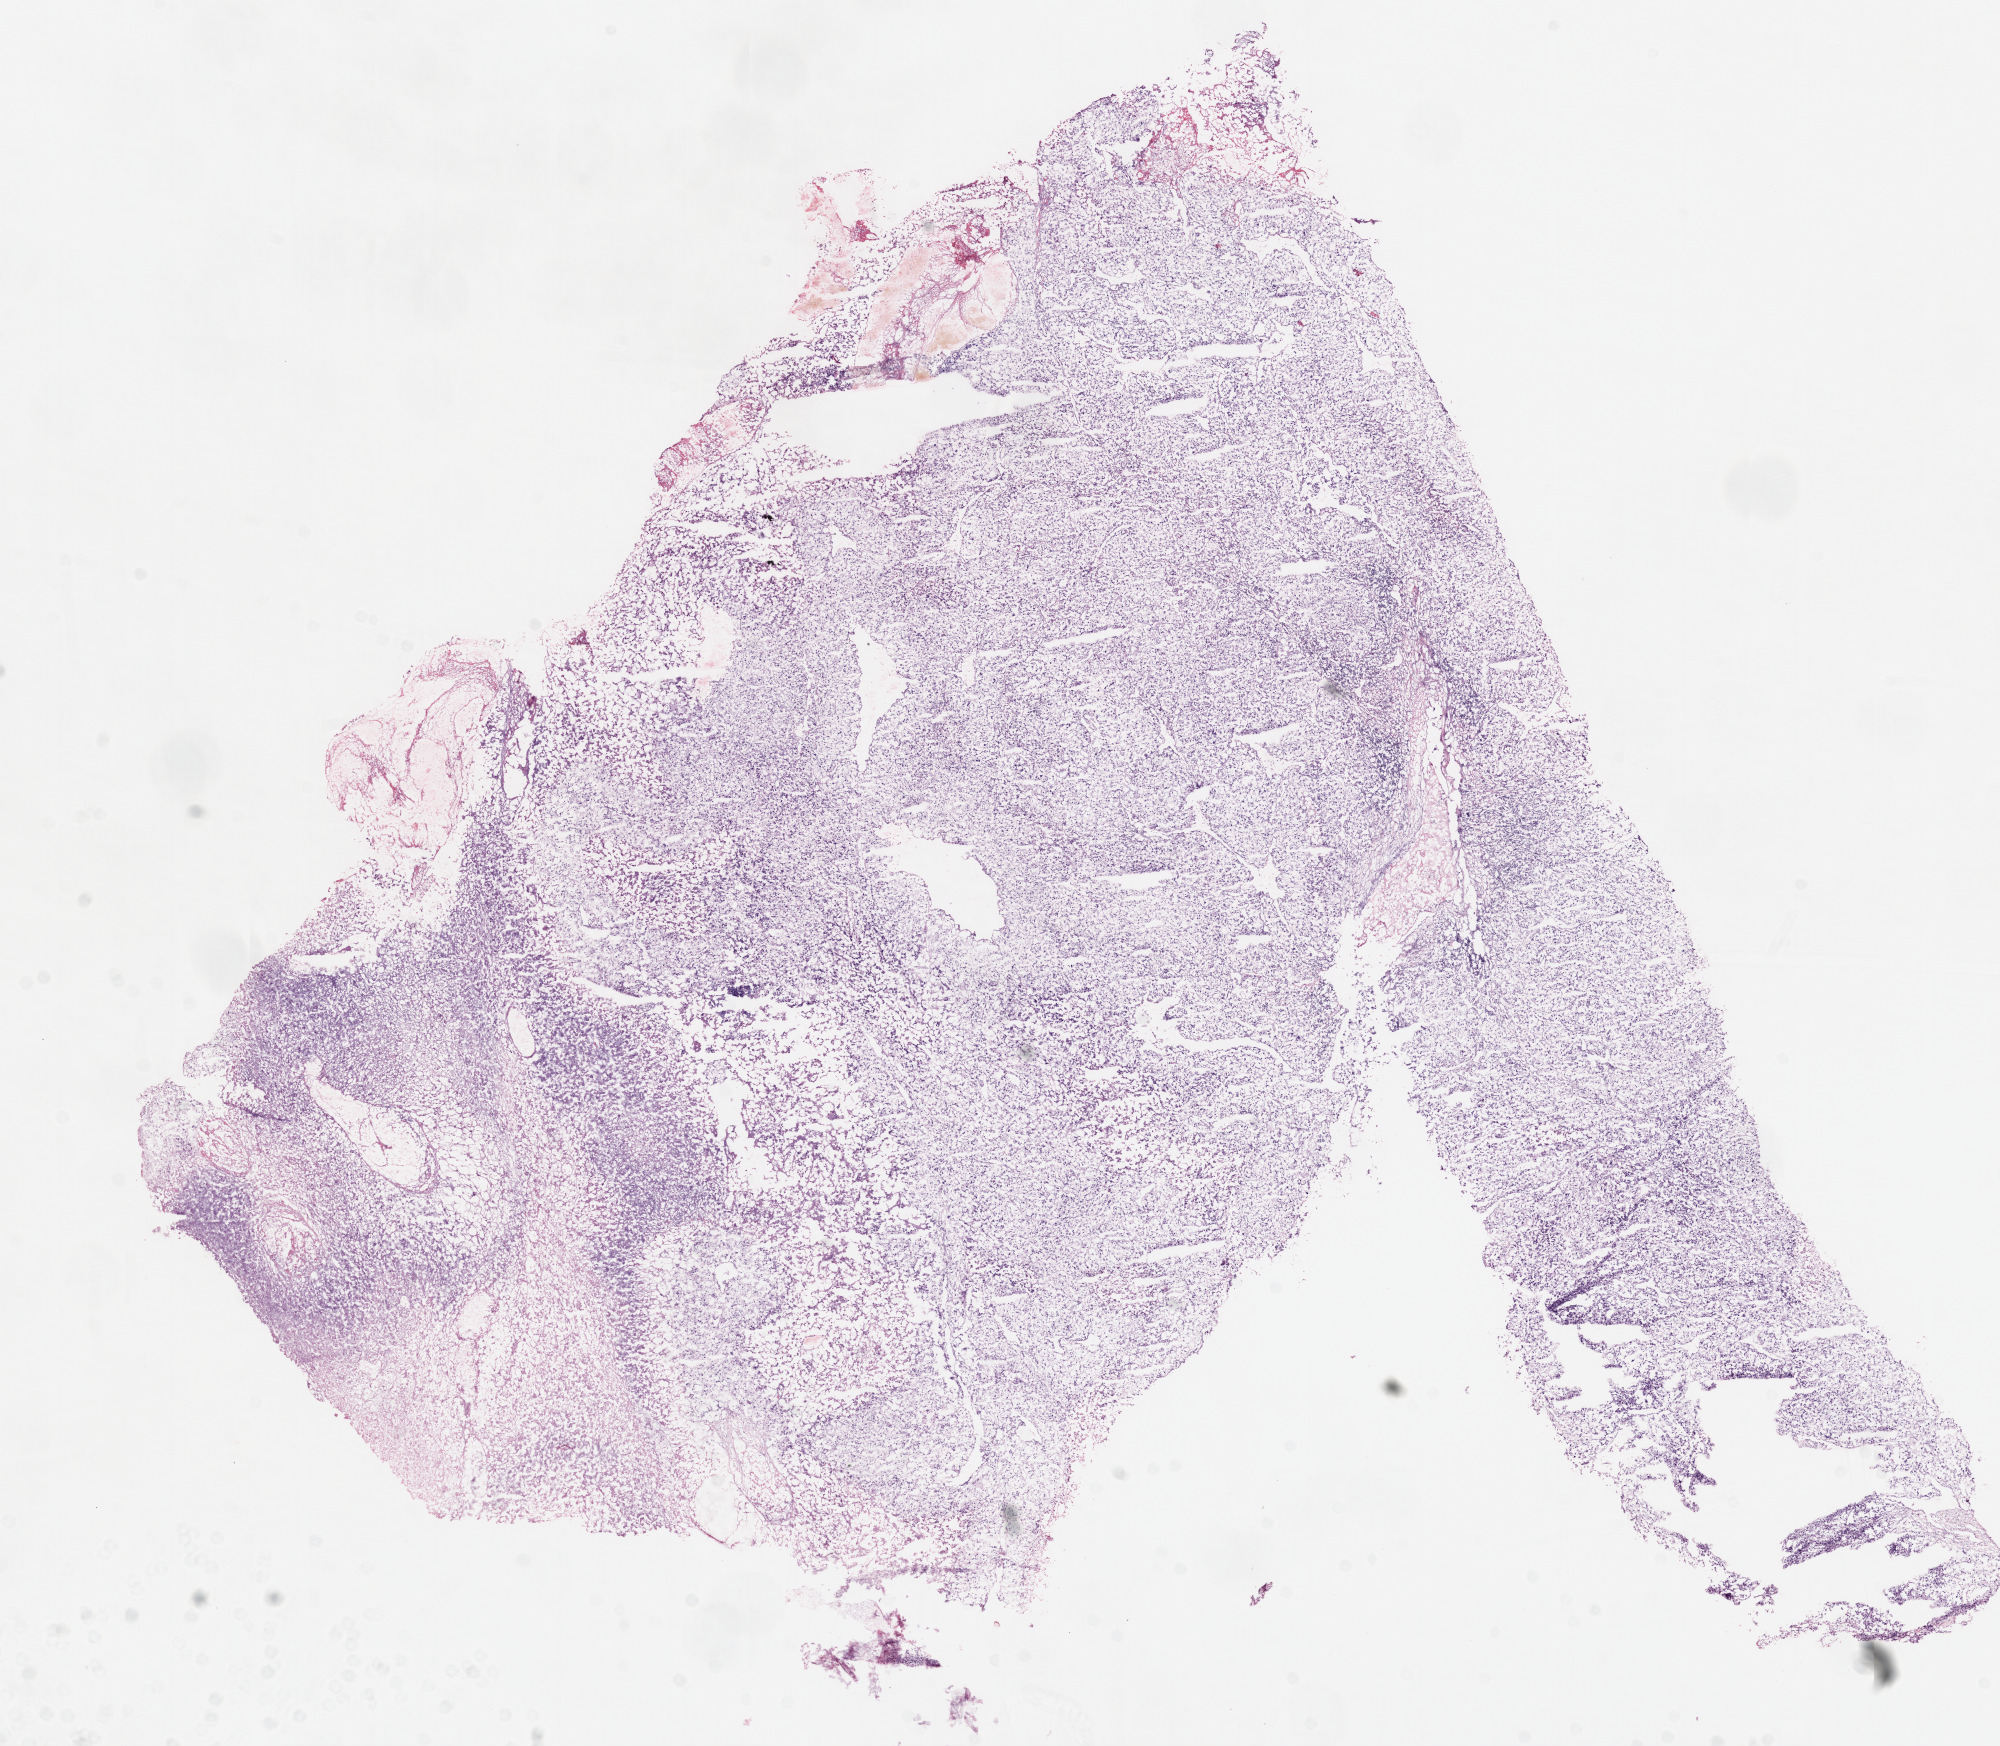
H&E whole-slide image — a low-resolution overview of the entire scanned area, about 16.0 x 14.0 mm; frozen section; primary tumour sample from the kidney. Male, age 39 years at initial diagnosis. Histologic grade: G4 (undifferentiated). Pathologist review of this section (percent, as recorded): tumour cells 80%, tumour nuclei 90%, normal cells 0%, stromal cells 10%, necrosis 10%.
- laterality: left
- AJCC pathologic stage: II
- diagnosis: Clear cell adenocarcinoma, NOS